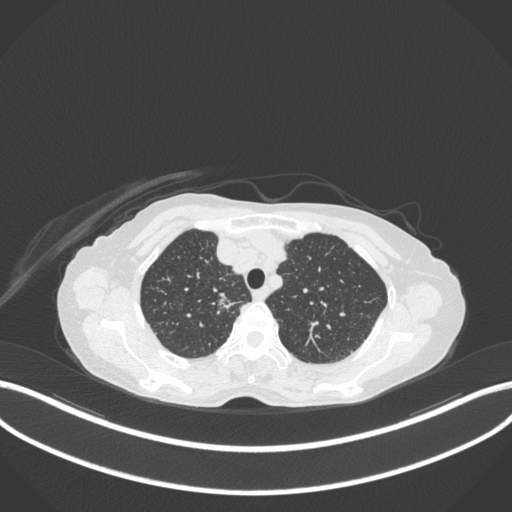
Chest CT, one axial slice; position 301 of 363 along the scan axis; 120 kVp; lung window (W 1500 / L -600 HU); 512 × 512 image matrix. Female patient, age 75 years. From the clinical record (not read from this slice): clinical TNM (as recorded): T1c N1 M1.
Annotated regions visible in this slice (bounding box drawn by a radiologist):
- lung tumour (recorded histology: adenocarcinoma): bounding box (x1, y1, x2, y2) in pixels: (212, 291, 249, 314)